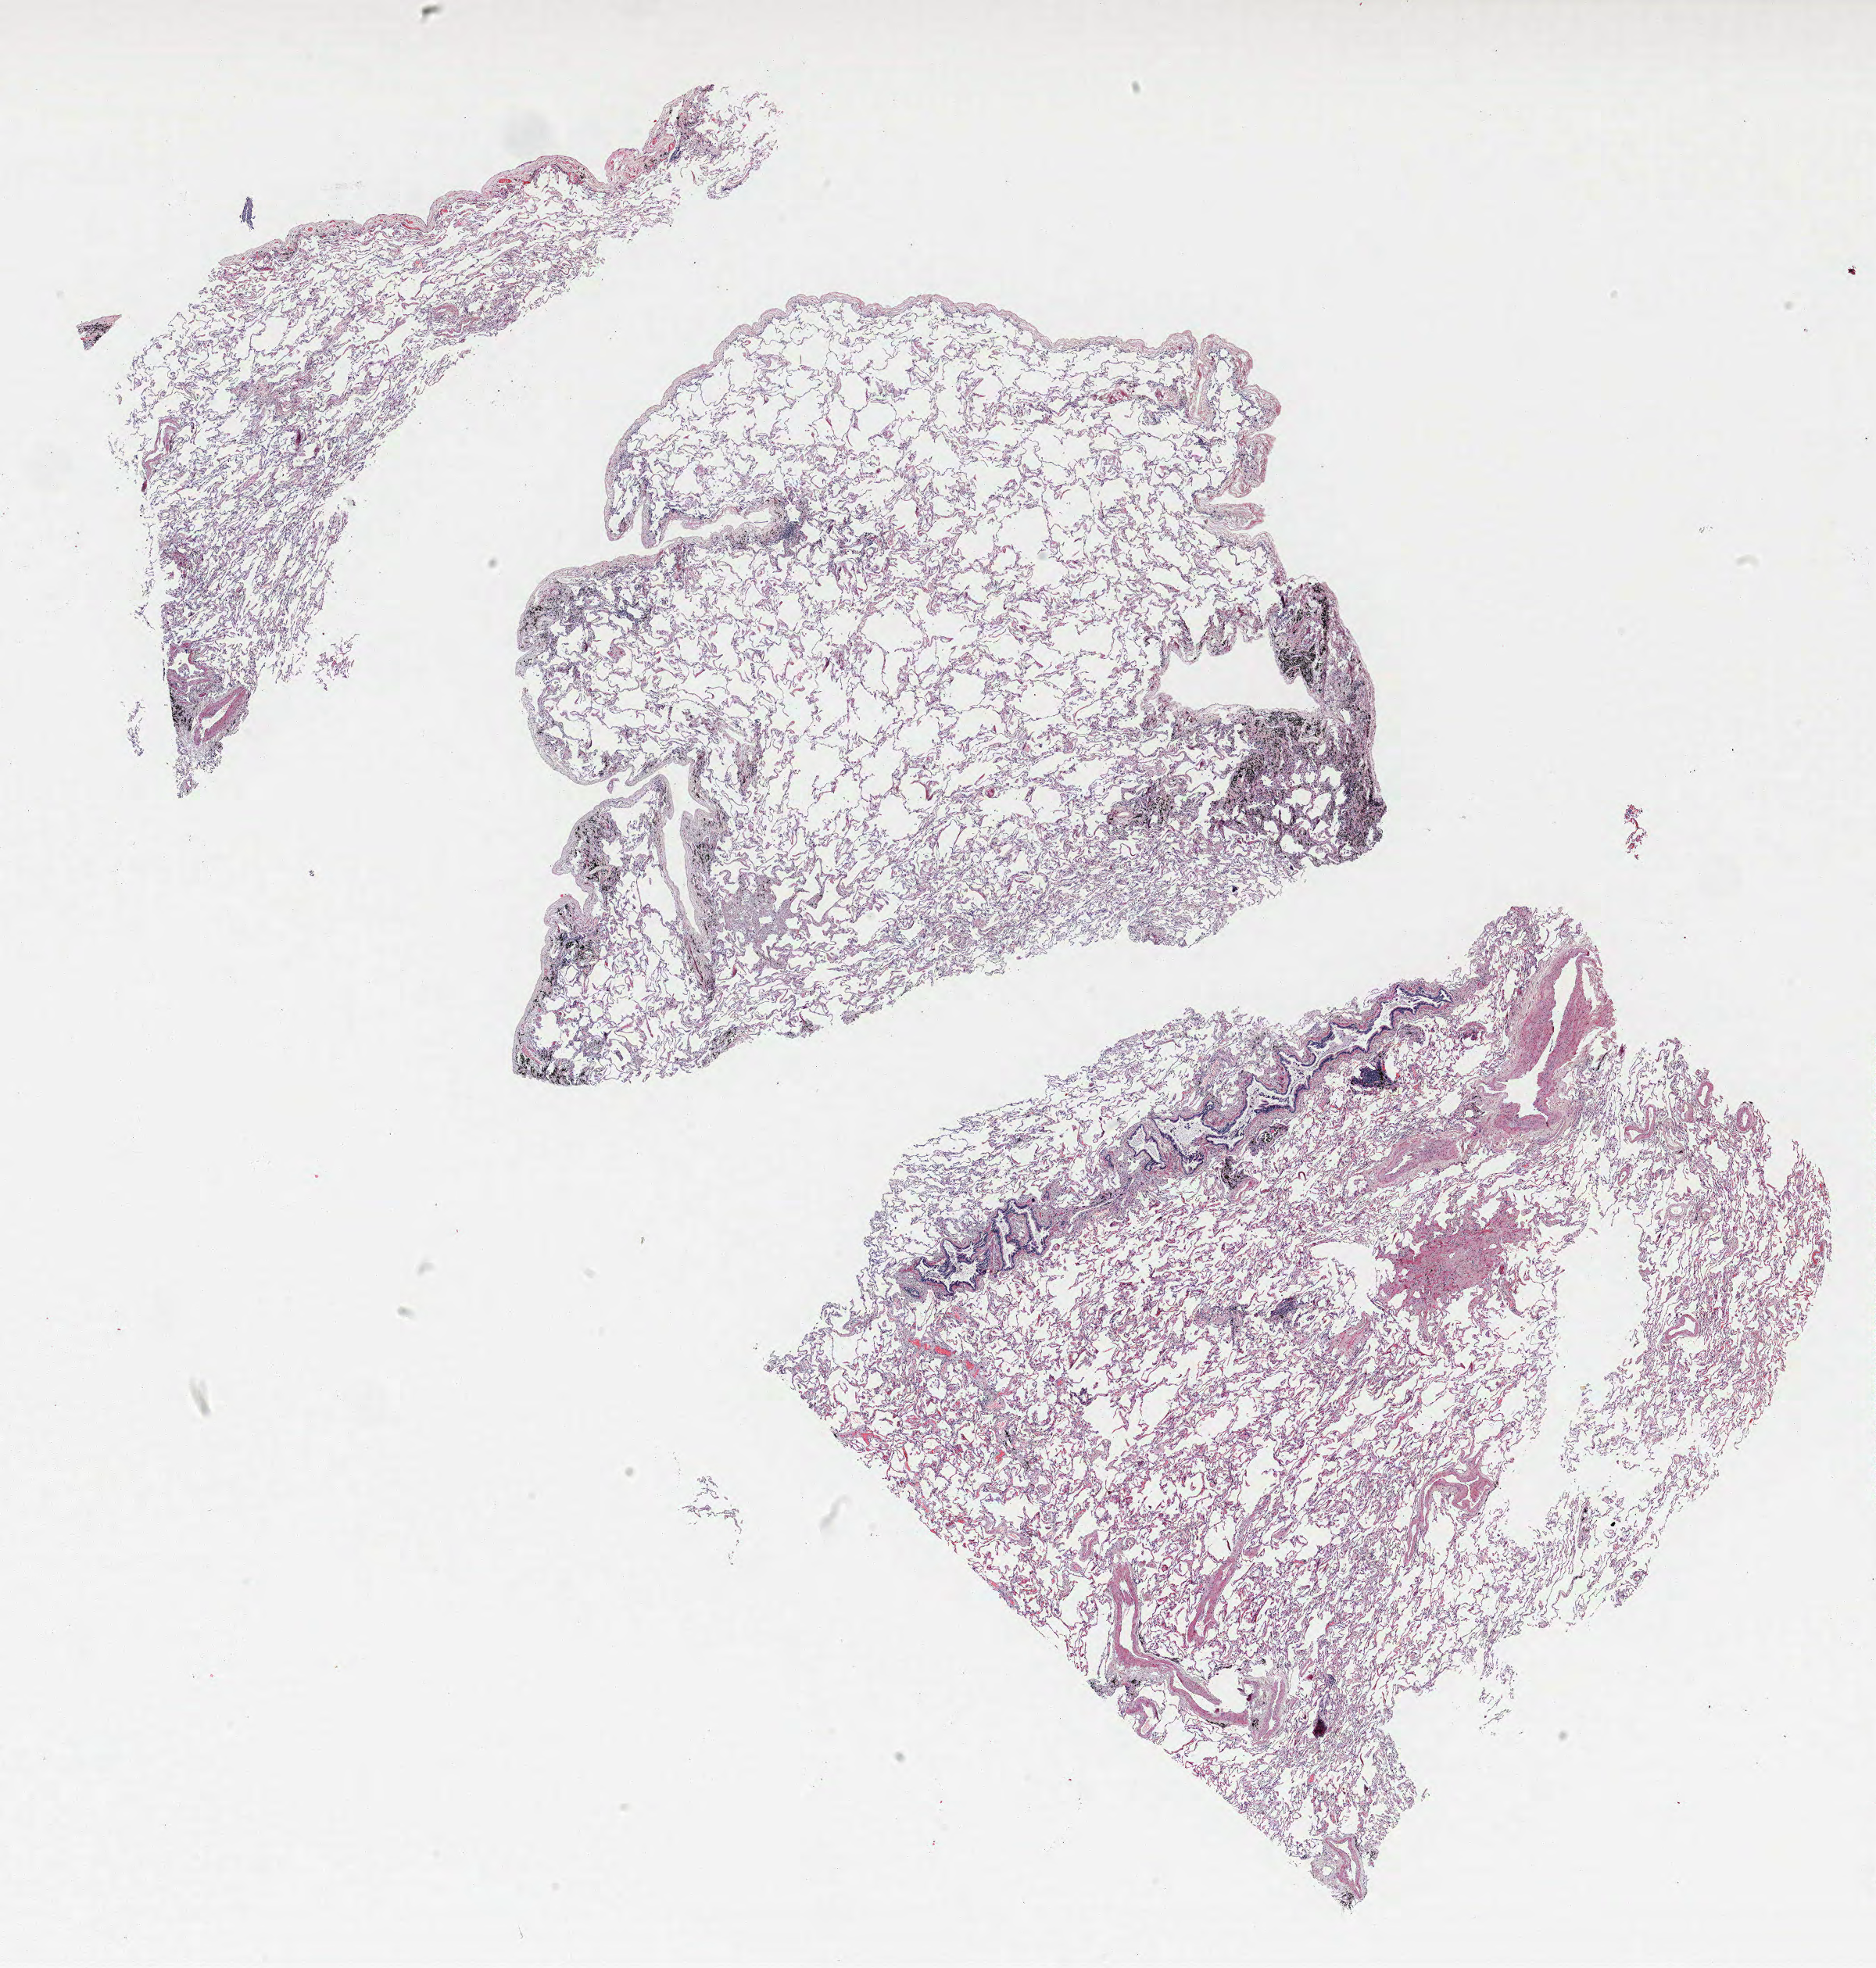
Whole-slide histology image, H&E-stained — whole scanned area (about 19.2 x 20.1 mm, slide scanned at 40x) shown as a low-resolution overview. FFPE section. Lung. Male, age 70 at enrolment. Former smoker at enrolment. Grade: poorly differentiated (G3).
* participant's lung-cancer diagnosis: Squamous cell carcinoma, NOS
* stage (AJCC 6th edition): IA
* primary tumour location (clinical record): right upper lobe
* tumour size (pathology): 18 mm